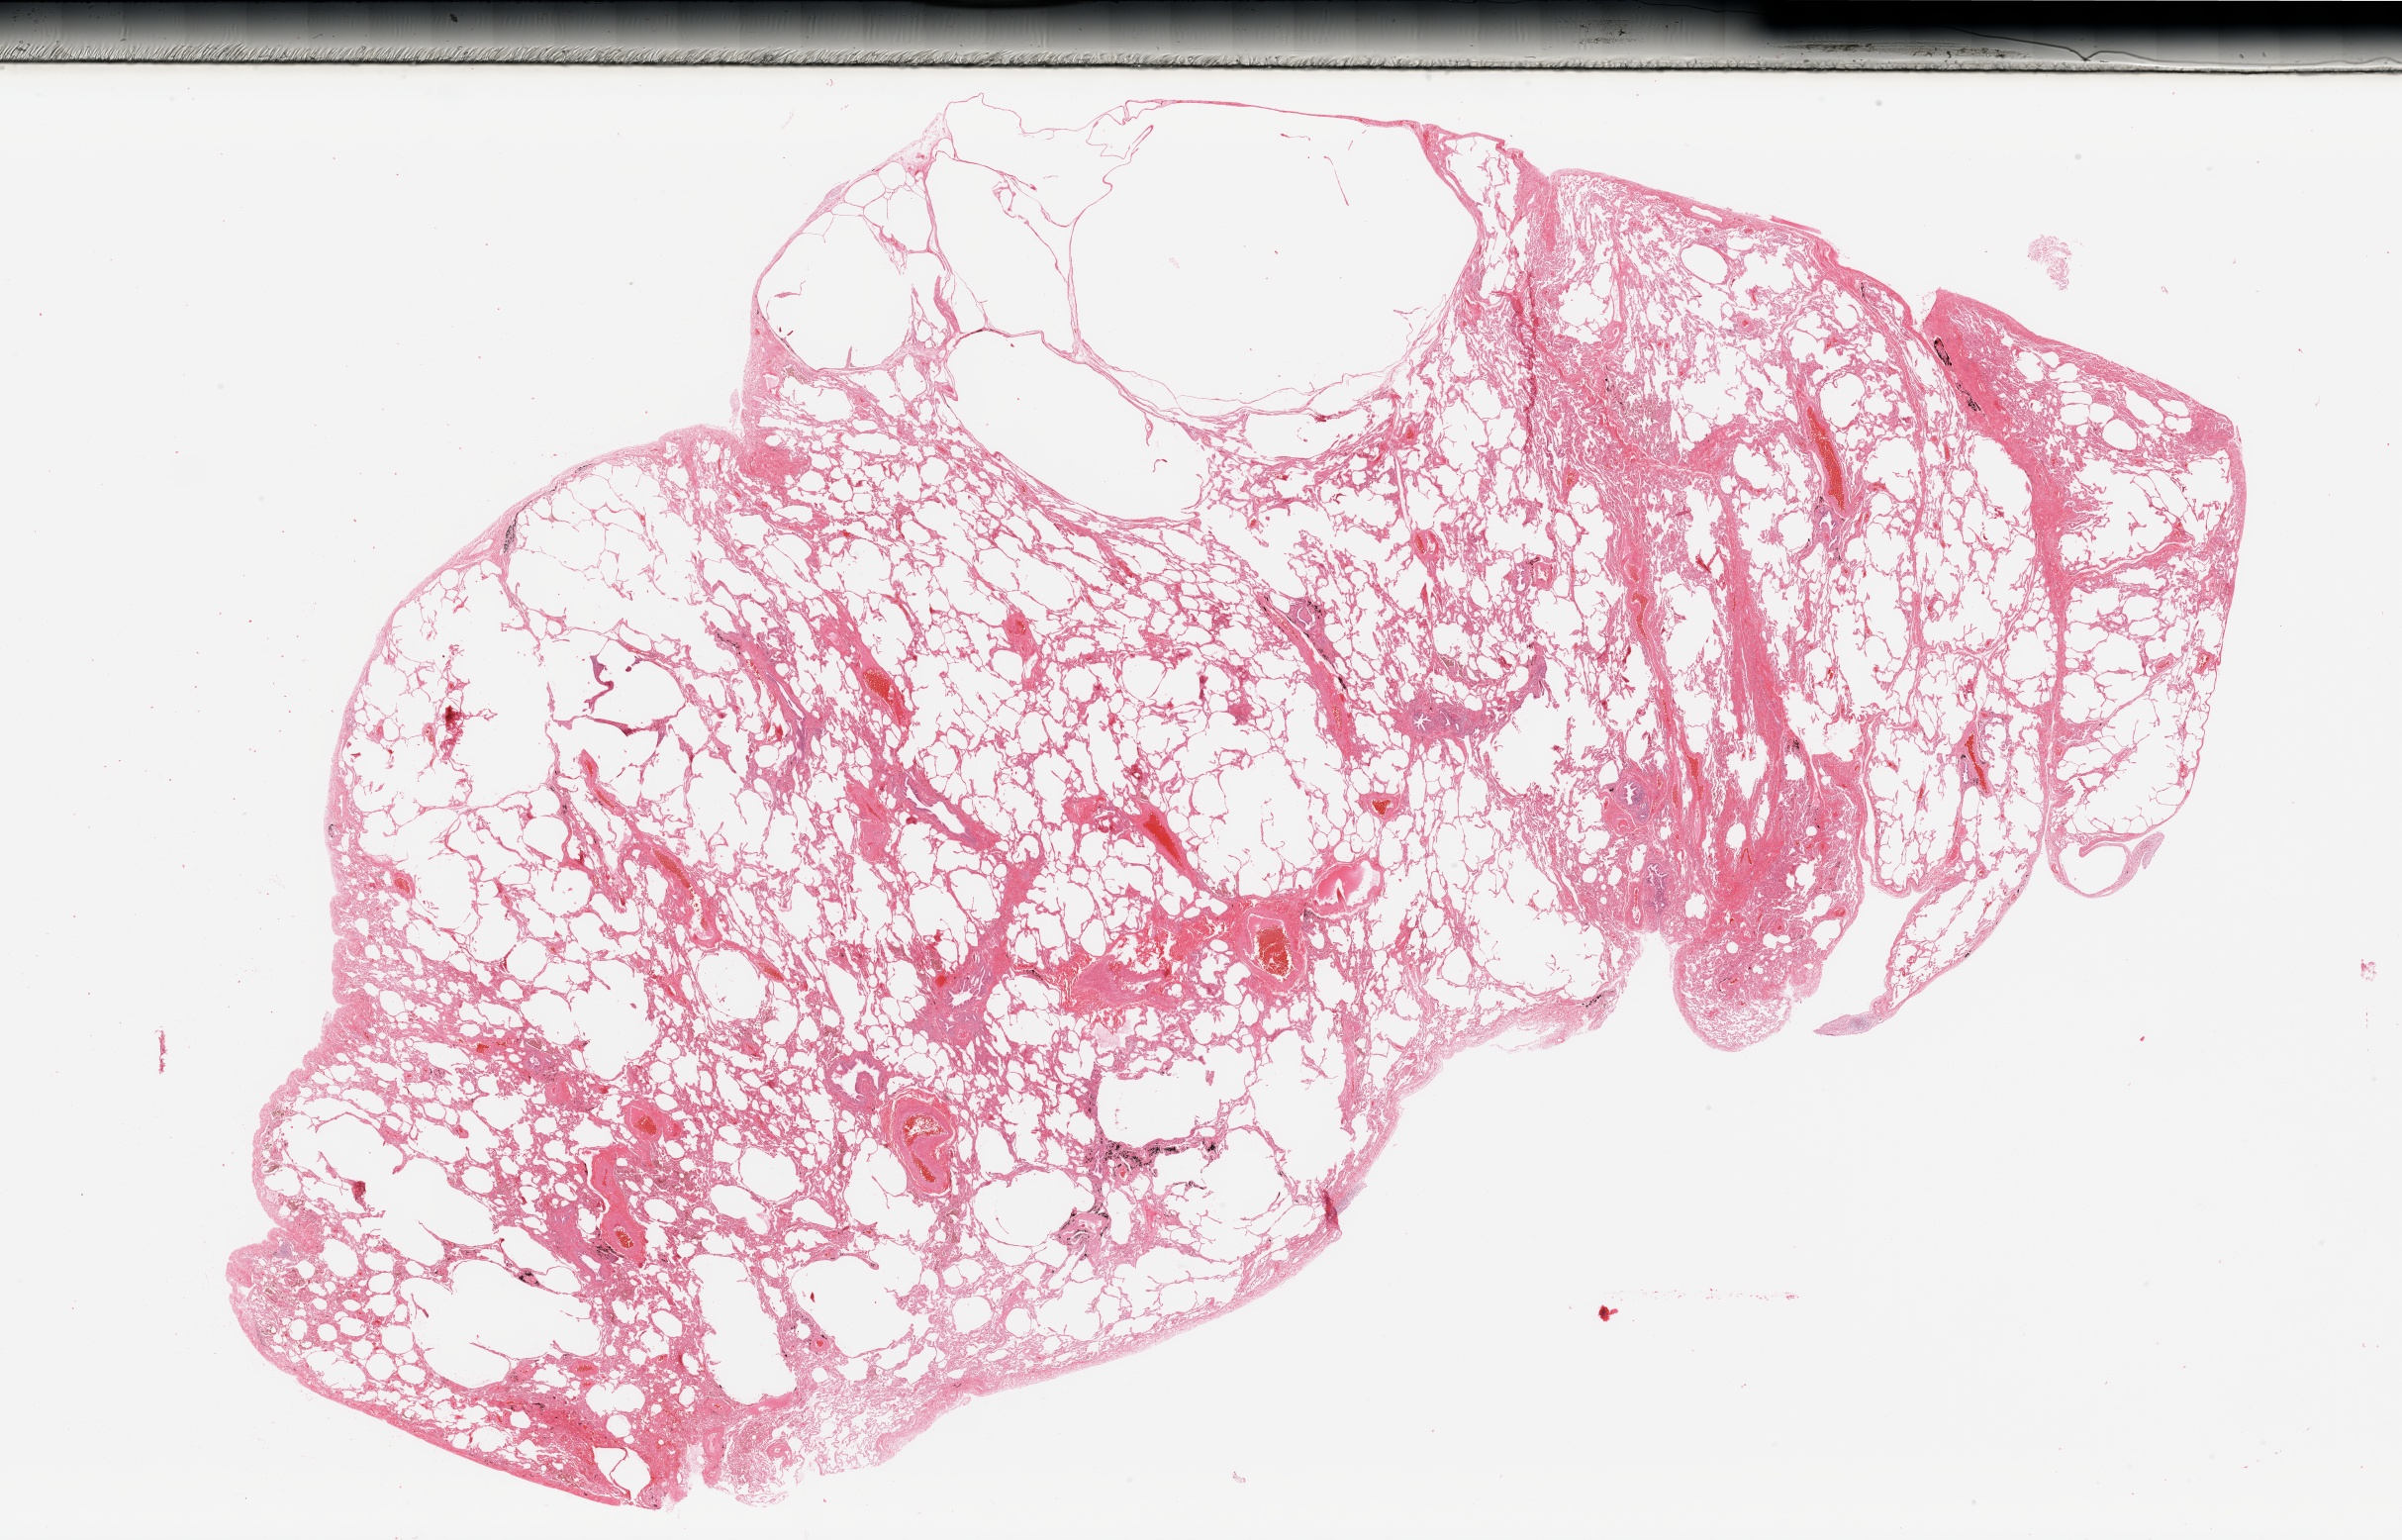
Digitized H&E-stained tissue section (whole slide) — whole scanned area (about 38.4 x 24.6 mm, acquisition: 20x scan) shown as a low-resolution overview; normal (non-tumour) tissue sample, lung. Patient: male, age 59 years.
* this section: normal (non-tumour) tissue from the same patient
* patient diagnosis: Adenocarcinoma, NOS